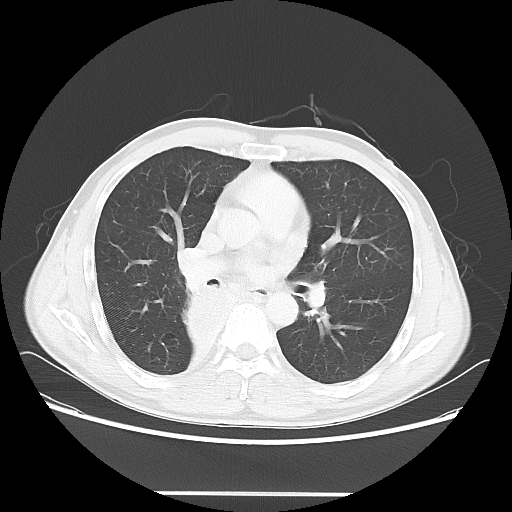
Chest CT, one axial slice; slice 34 of 62 in the series (ordered by position); reconstruction kernel LUNG; 120 kVp; lung window (W 1500 / L -600 HU); 5 mm slice thickness; 512 × 512 image matrix. Male patient, age 47 years. From the clinical record (not read from this slice): clinical TNM (as recorded): T2 N0 M0; histopathological grade: G2.
Outlined on this slice (rectangle marked by the reading radiologist):
- lung tumour (recorded histology: squamous cell carcinoma): bounding box [x1, y1, x2, y2] px = [181, 278, 234, 356]